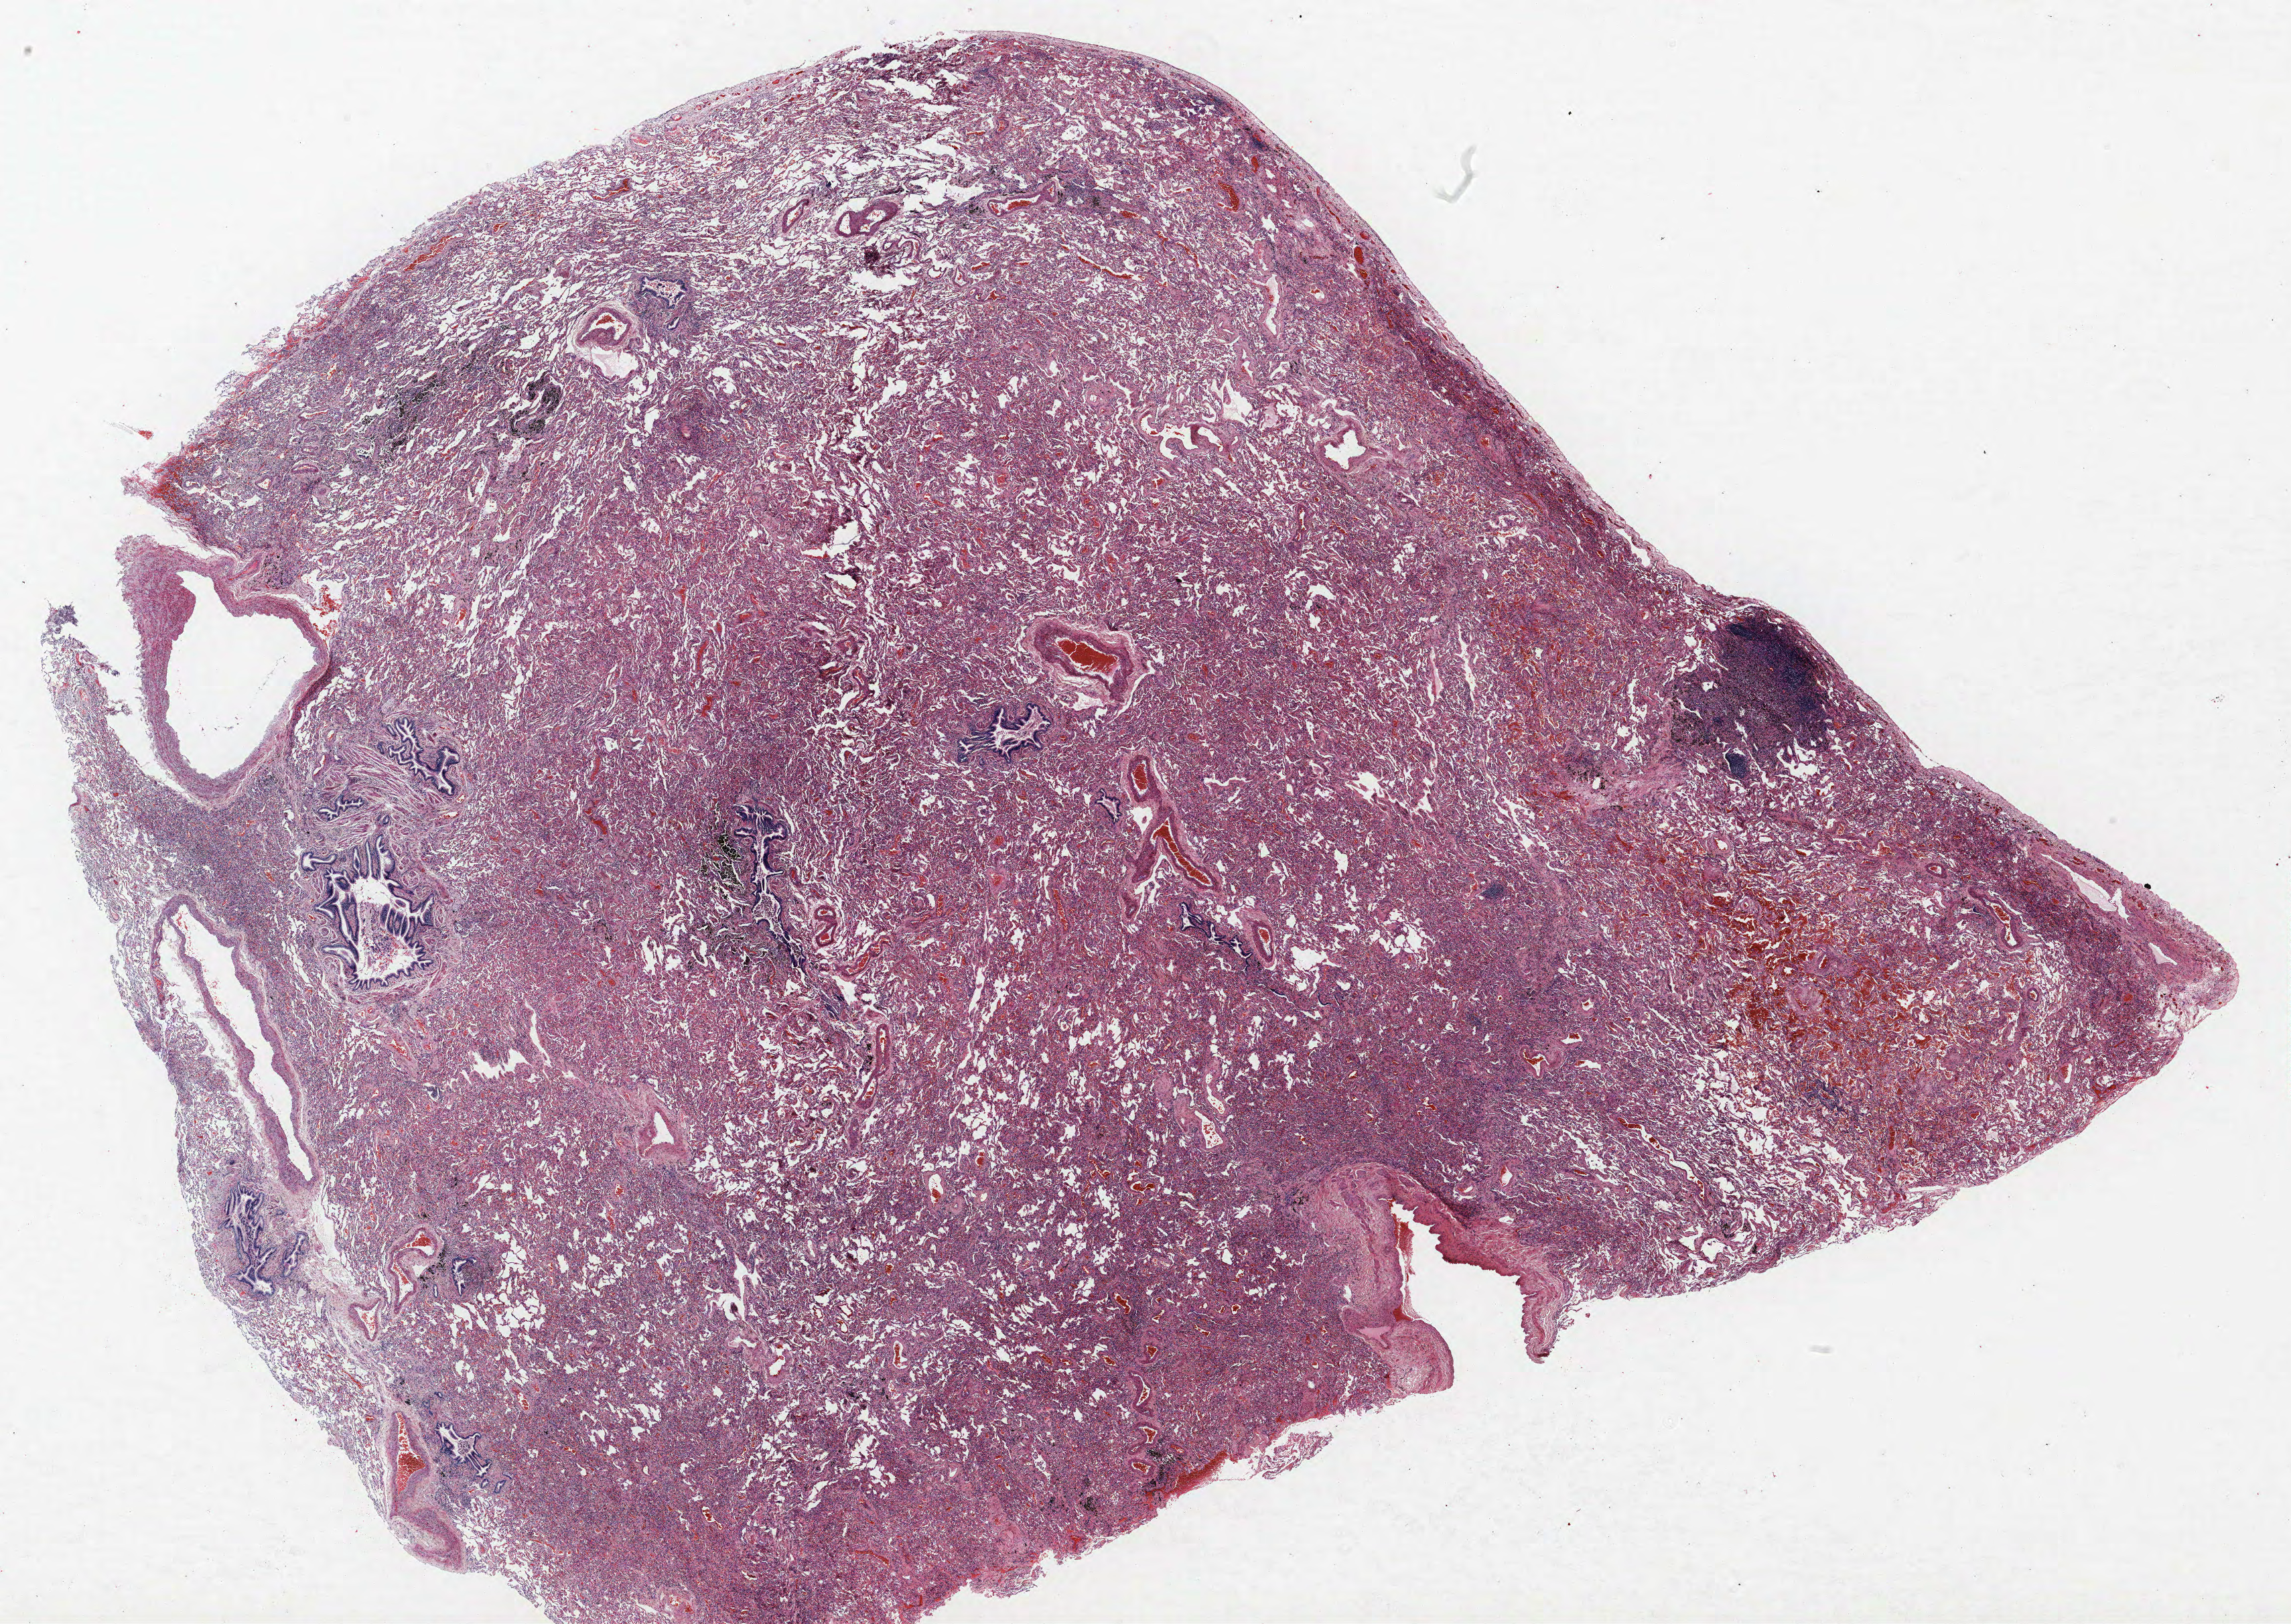
H&E-stained whole-slide image, whole scanned area (about 27.4 x 19.4 mm, from a 40x scan) shown as a low-resolution overview. Formalin-fixed paraffin-embedded (FFPE) section. Lung. Female, age 60 at enrolment. Former smoker at enrolment. Grade: poorly differentiated (G3).
- participant's lung-cancer diagnosis: Non-small cell carcinoma
- stage (AJCC 6th edition): IB
- tumour size (pathology): 16 mm
- primary tumour location (clinical record): left upper lobe